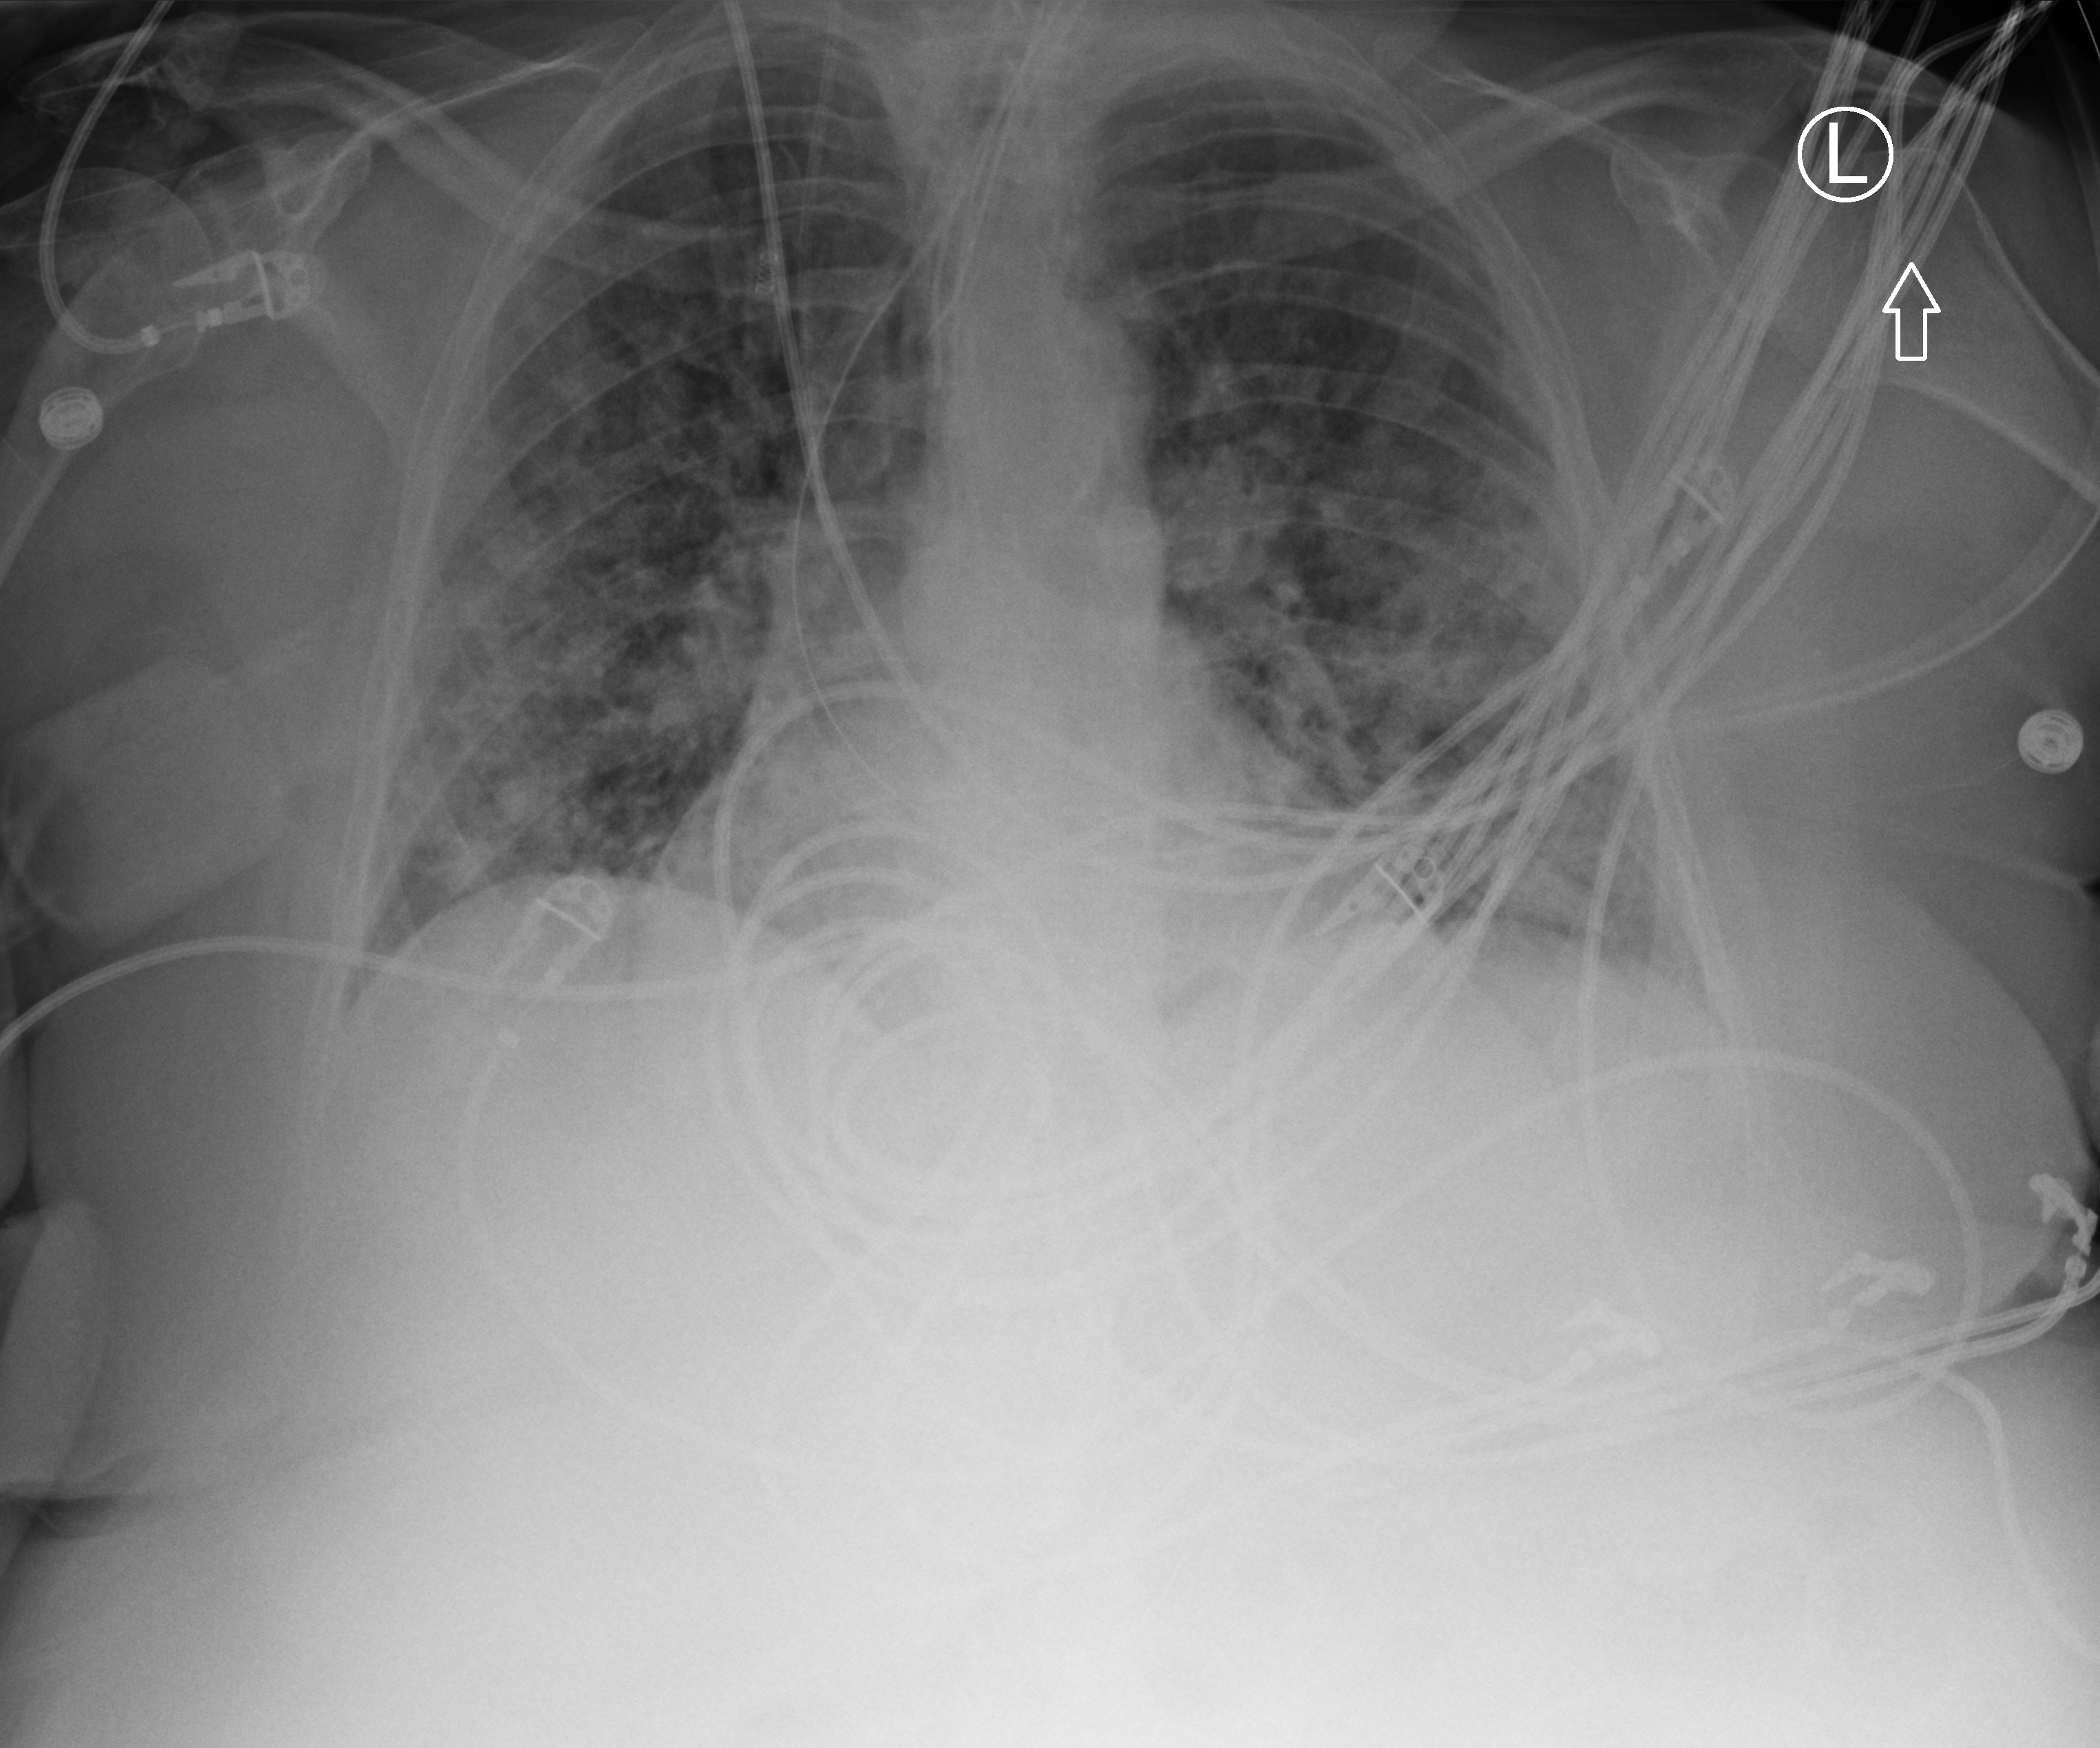
Portable chest radiograph, anteroposterior (AP) projection. Patient hospitalised with COVID-19; female, aged 75–90 years.
From the hospital-stay record, not from the radiograph (when in the stay this image was taken is not recorded): chronic kidney disease (admission record): no.